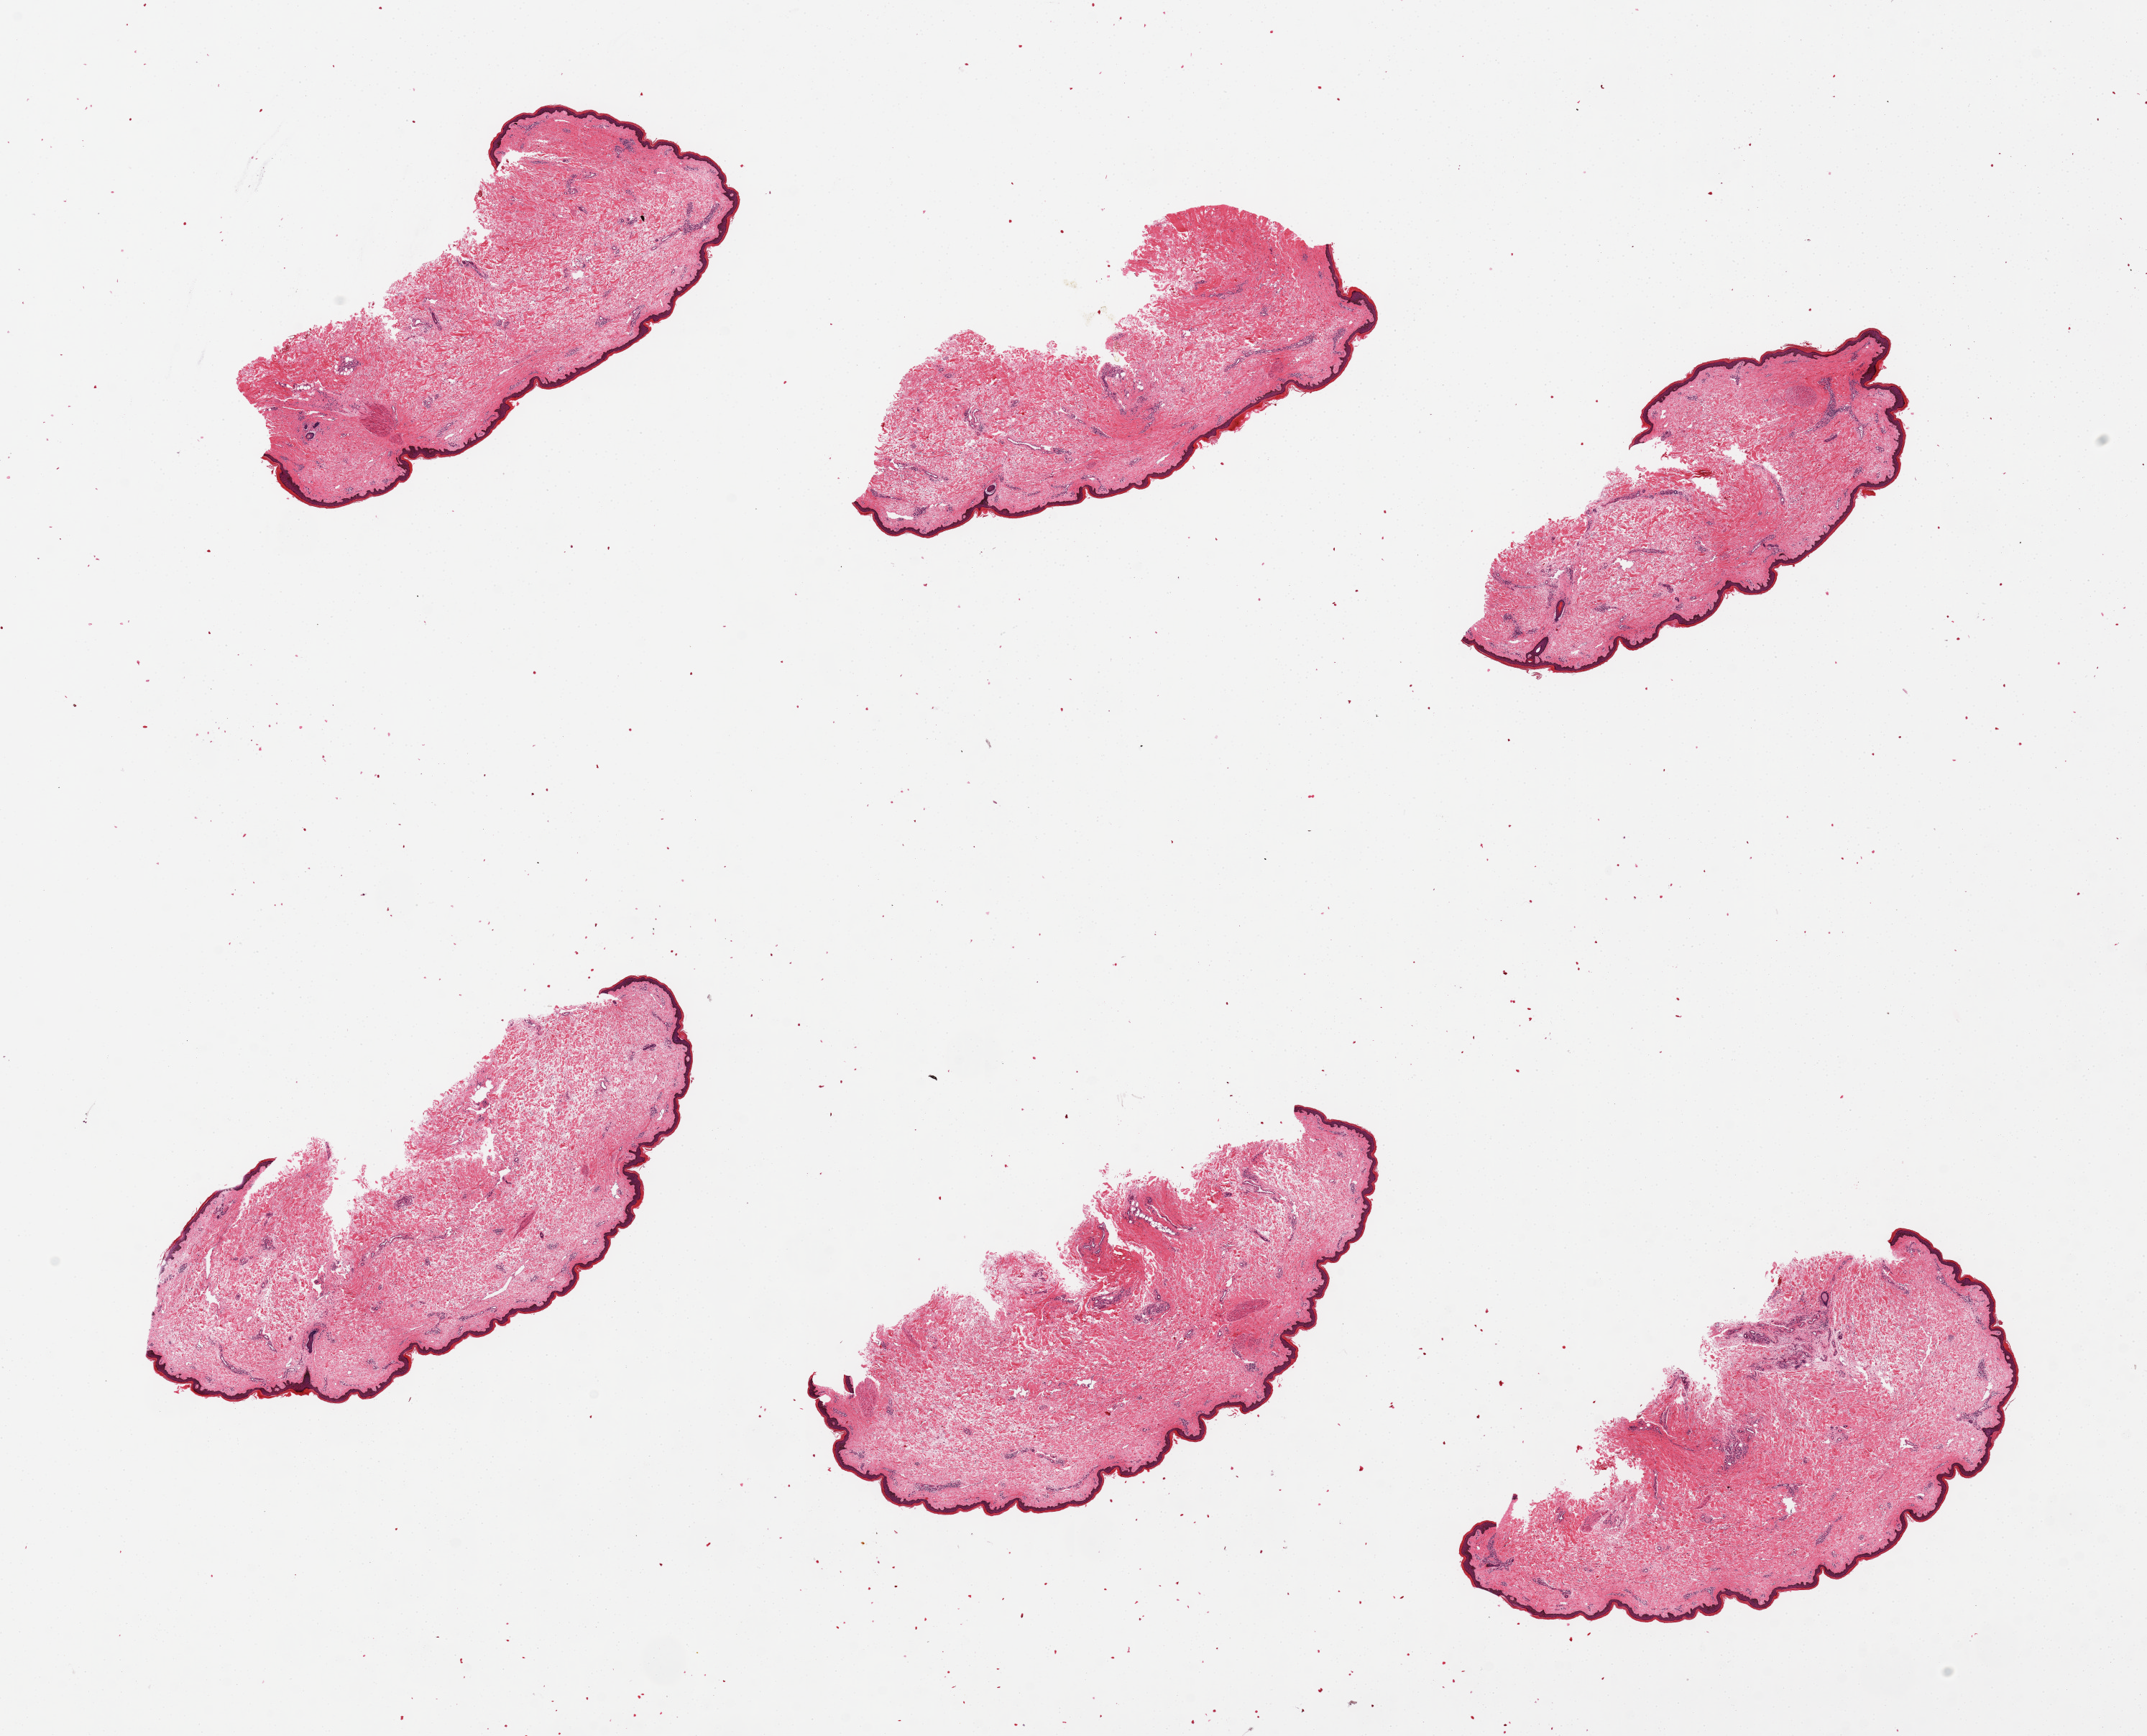
Whole-slide image, H&E stain, brightfield, whole scanned area (about 23.6 x 19.1 mm) shown as a low-resolution overview, PAXgene-fixed, paraffin-embedded tissue, target tissue: skin of lower leg, tissue donor sample. Female donor.
Review note (as recorded): 6 pieces, minimal fat, squamous epithelium is ~50-70 microns.